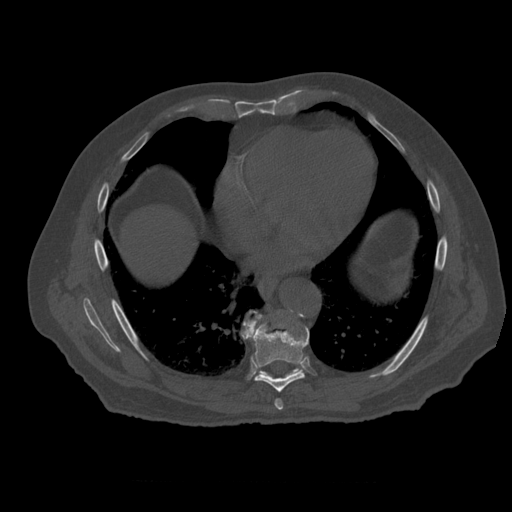
CT including the spine, one axial slice; slice 337 of 399 in the series (ordered by position); 120 kVp; bone window (W 1800 / L 400 HU); 1.25 mm slice thickness; 512 × 512 image matrix, field of view 407 × 407 mm. Patient age 73 years. Case-level facts recorded for this patient, not image findings: primary cancer: prostate; vertebrae with lytic lesions (as recorded): L2.
Annotated regions visible in this slice (semi-automatic segmentation, software-assisted and operator-edited):
- T7 vertebra: bounding box <275,399,283,411> (left, top, right, bottom; pixels)
- T8 vertebra: <243,316,310,393>
- T9 vertebra: <243,311,300,378>